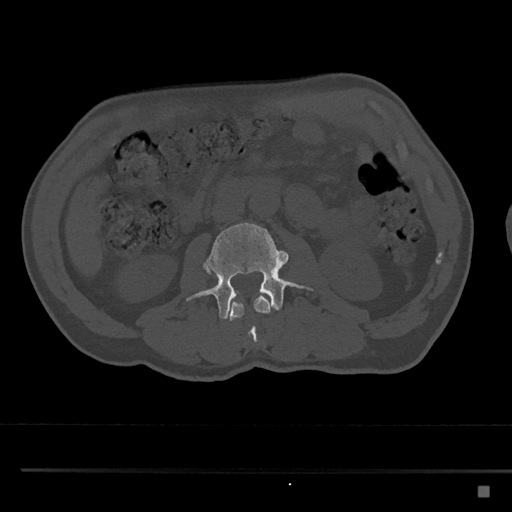
CT including the spine, one axial slice; position 717 of 797 along the scan axis; 120 kVp; bone window (W 1800 / L 400 HU); 0.5 mm slice thickness; 512 × 512 image matrix. Patient: male, 59 years. From the clinical record (not read from this slice): primary cancer: prostate.
Structures marked on this image (semi-automatic segmentation, software-assisted and operator-edited):
- L2 vertebra: bounding box [x1, y1, x2, y2] px = [208, 272, 271, 342]
- L3 vertebra: [185, 222, 314, 319]